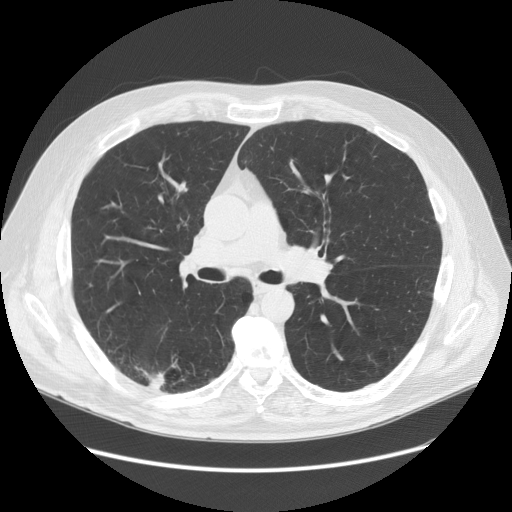
Low-dose screening chest CT, one axial slice. Slice 86 of 149 in the series (ordered by position). Reconstruction kernel STANDARD. 120 kVp. Lung window (W 1500 / L -600 HU). 512 × 512 image matrix, field of view 400 × 400 mm.
Annotated regions visible in this slice (manually delineated by an expert):
- lesion 1 (tumor, lower lobe of right lung): bounding box (x1, y1, x2, y2) in pixels: (147, 372, 165, 389)